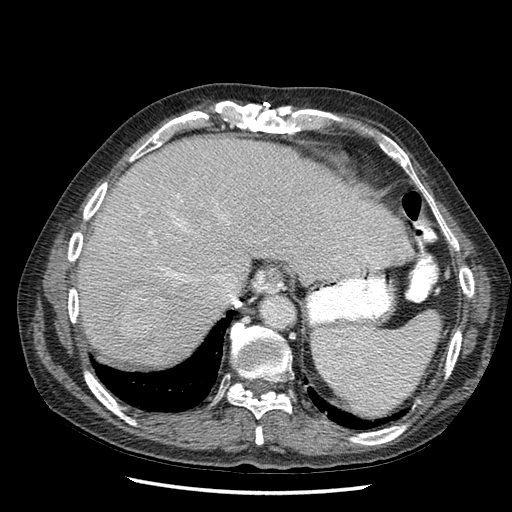
Contrast-enhanced abdominal CT (liver protocol), one axial slice. Position 46 of 67 along the scan axis. Reconstruction kernel STANDARD. Soft-tissue window (W 400 / L 40 HU). 2.5 mm slice thickness. 512 × 512 image matrix, field of view 360 × 360 mm. From the clinical record (not read from this slice): diagnosis: hepatocellular carcinoma (patient treated with transarterial chemoembolisation; whether this scan precedes or follows treatment is not stated here); TNM stage (as recorded): Stage-I; Child-Pugh class: A.
Annotated regions visible in this slice (semi-automatic segmentation, software-assisted and operator-edited):
- liver parenchyma outside the tumour (the mass and vessels are separate outlines, so this box may not span the whole liver): bounding box <78,136,412,370> (left, top, right, bottom; pixels)
- mass: <111,288,166,340>
- liver vessels: <138,218,160,247>